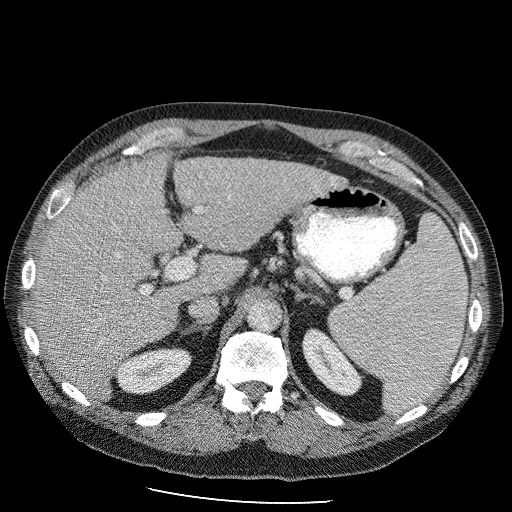
Contrast-enhanced abdominal CT (liver protocol), one axial slice; 120 kVp; soft-tissue window (W 400 / L 40 HU); 2.5 mm slice thickness; 512 × 512 image matrix, field of view 400 × 400 mm. From the clinical record (not read from this slice): diagnosis: hepatocellular carcinoma (patient treated with transarterial chemoembolisation; whether this scan precedes or follows treatment is not stated here); TNM stage (as recorded): Stage-II; Child-Pugh class: B; tumour differentiation: moderately differentiated; tumour nodularity: uninodular.
Outlined on this slice (semi-automatic segmentation, software-assisted and operator-edited):
- liver parenchyma outside the tumour (the mass and vessels are separate outlines, so this box may not span the whole liver): box from (x=34, y=152) to (x=354, y=402) px
- liver vessels: (x=107, y=199)–(x=213, y=337)